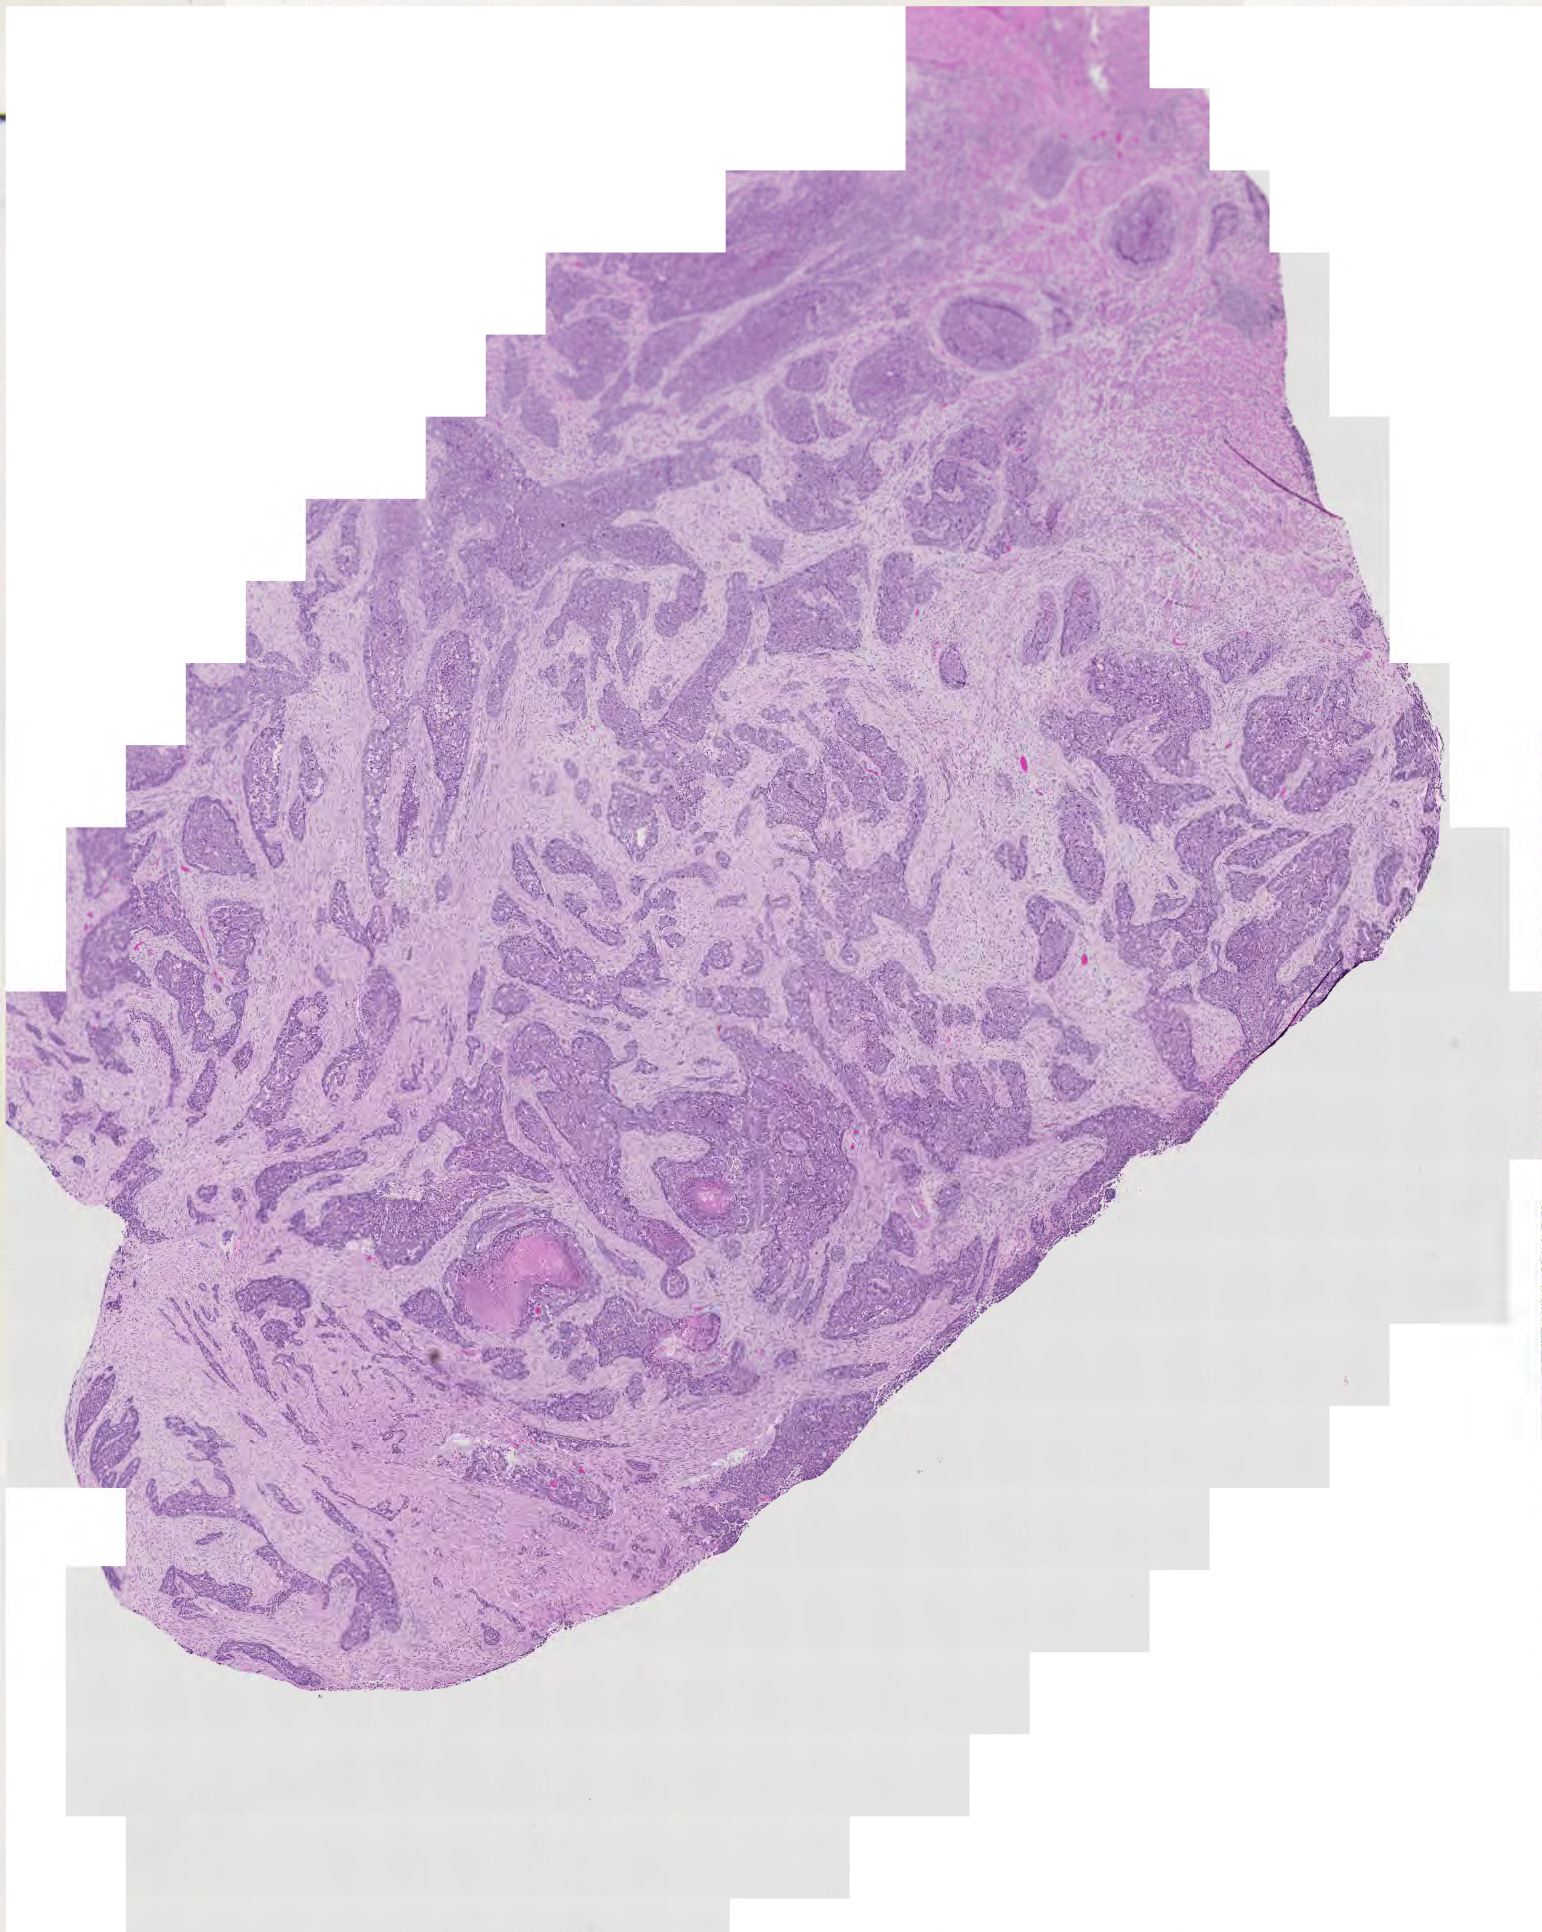
Digitized H&E-stained tissue section (whole slide), whole scanned area (about 8.0 x 10.0 mm, acquisition: 20x scan) shown as a low-resolution overview. Uterus, tumour tissue. Patient: female, age 65 years. Histologic grade: G3 (poorly differentiated).
* AJCC pathologic stage: IV
* diagnosis: Endometrioid adenocarcinoma, NOS